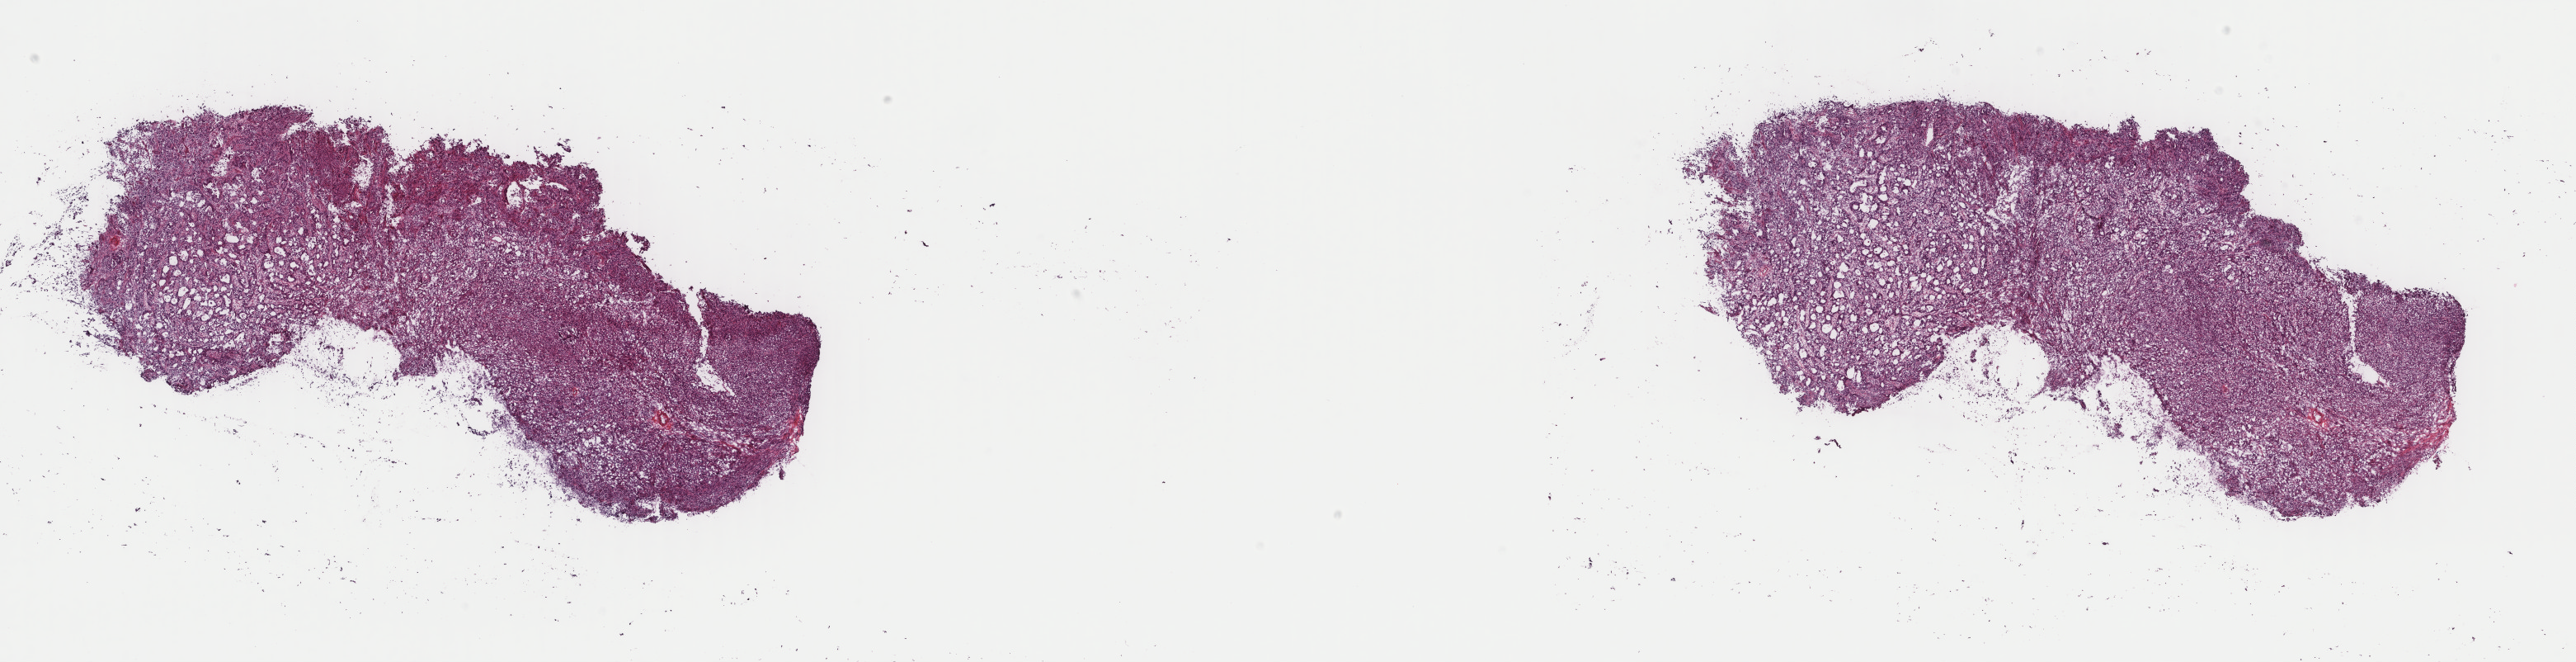
Whole-slide histology image, H&E, a low-resolution overview of the entire scanned area, about 24.8 x 6.4 mm (slide scanned at 40x); frozen section from the top of the tissue portion; cervix, primary tumour sample. Female patient; age at initial diagnosis 40 years. Composition of this section per pathologist review: tumour cells 100%, tumour nuclei 90%.
Pathologic diagnosis: Adenocarcinoma, endocervical type (cervix uteri).